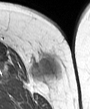
MRI of an extremity soft-tissue mass, one axial slice; position 10 of 45 along the scan axis; MR volume resampled by the dataset authors to the PET/CT grid (not the native acquisition matrix); 3.27 mm slice thickness; 90 × 109 image matrix, field of view 88 × 106 mm. Female patient. Case-level facts recorded for this patient, not image findings: histological type: leiomyosarcoma; grade: intermediate; site of the primary tumour: parascapusular.
Outlined on this slice (expert contour drawn on MRI and transferred to this co-registered scan by the dataset authors):
- gross tumour volume including surrounding oedema: bounding box [x1, y1, x2, y2] px = [31, 55, 61, 79]
- gross tumour volume (mass): [33, 57, 59, 76]